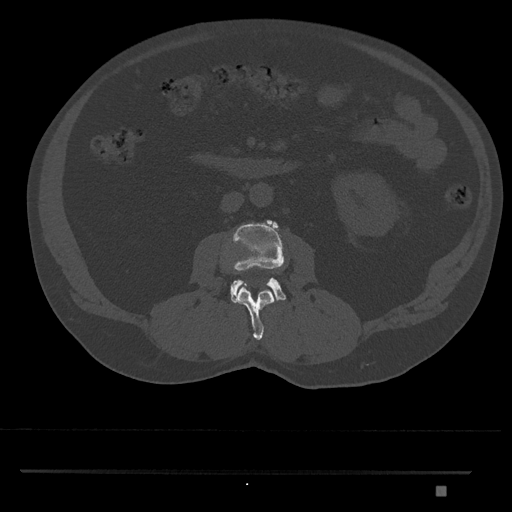
CT including the spine, one axial slice; position 718 of 1134 along the scan axis; reconstruction kernel Br40s/3; 120 kVp; bone window (W 1800 / L 400 HU); 0.5 mm slice thickness; 512 × 512 image matrix, field of view 429 × 429 mm. Patient: male, 65 years. Case-level facts recorded for this patient, not image findings: primary cancer: prostate.
Outlined on this slice (semi-automatically segmented with operator editing):
- L2 vertebra: box from (x=236, y=286) to (x=275, y=340) px
- L3 vertebra: (x=225, y=220)–(x=286, y=303)